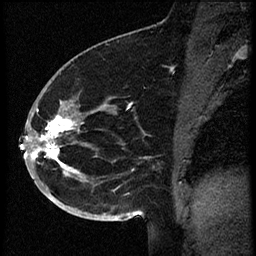
Breast MRI (dynamic contrast-enhanced), one sagittal slice; slice 36 of 60 in the series (ordered by position); dynamic contrast-enhanced study with each time point stored as its own series, time point 2 of 3 at this slice position (early post-contrast, ordered by acquisition time); 1.5 T; TE 4.2 ms, TR 18.9 ms; 2 mm slice thickness; 256 × 256 image matrix, field of view 200 × 200 mm. Female patient. From the clinical record (not read from this slice): setting: breast cancer imaged before/during neoadjuvant chemotherapy; receptor status: HR-positive, HER2-negative.
Structures marked on this image (semi-automatically segmented with operator editing):
- analysis volume of interest (the breast-tissue region the enhancement analysis was run in; not a lesion): bounding box (x1, y1, x2, y2) in pixels: (30, 87, 114, 173)
- tumour enhancement mask (voxels above the 100 % enhancement threshold inside the analysis volume of interest): (31, 109, 83, 167)